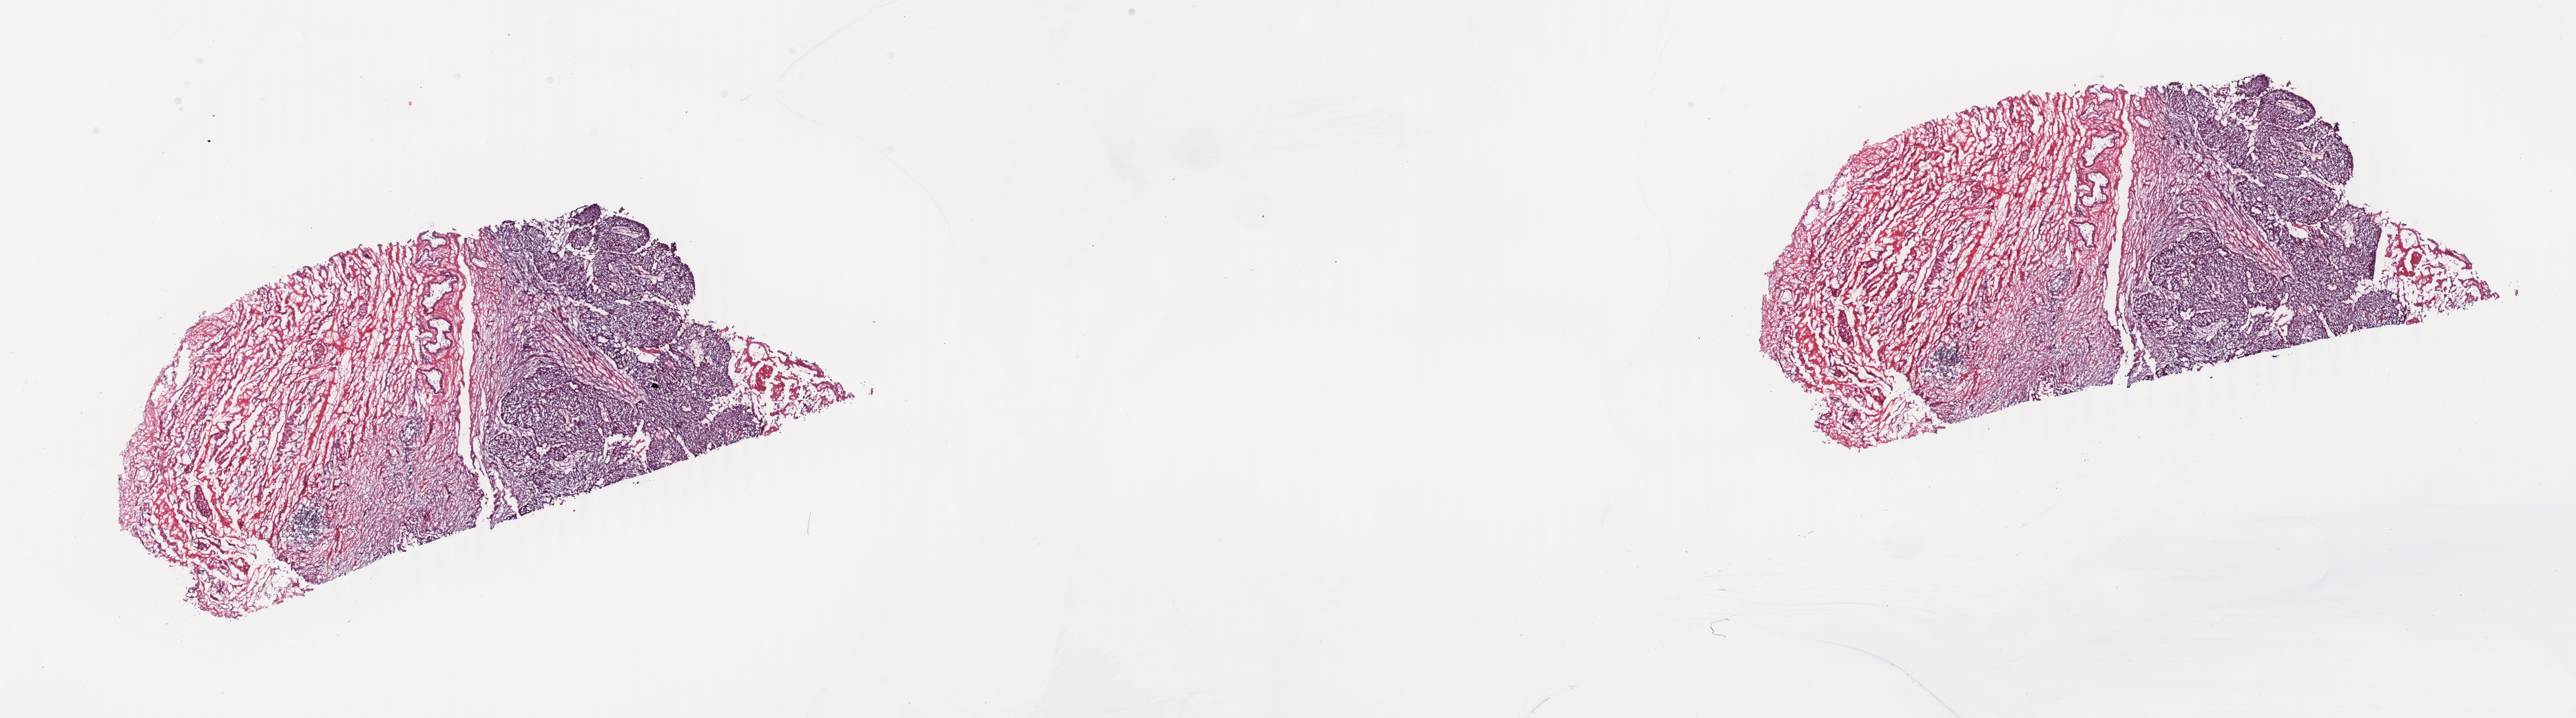
Whole-slide histology image, H&E-stained, whole scanned area (about 29.7 x 8.3 mm, slide scanned at 40x) shown as a low-resolution overview. Frozen section from the top of the tissue portion. Sample: primary tumour, cervix. Patient: female, age at initial diagnosis 59 years. Histologic grade: G2 (moderately differentiated). Composition of this section per pathologist review: tumour cells 60%, tumour nuclei 60%, normal cells 30%, stromal cells 10%, necrosis 0%. Inflammatory infiltration, as recorded: lymphocyte infiltration 5%, monocyte infiltration 0%, neutrophil infiltration 0%.
FIGO stage: IB1. Histologic diagnosis: Squamous cell carcinoma, NOS (cervix uteri).